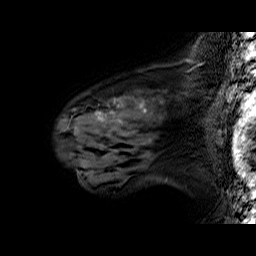
Breast MRI (dynamic contrast-enhanced), one sagittal slice. Slice 44 of 60 in the series (ordered by position). Dynamic contrast-enhanced series, time point 2 of 6 at this slice position (early post-contrast). 1.5 T. TE 6.4 ms, TR 32.9 ms. 4 mm slice thickness. 256 × 256 image matrix, field of view 200 × 200 mm. Female patient. Case-level facts recorded for this patient, not image findings: setting: breast cancer imaged before/during neoadjuvant chemotherapy; receptor status: HER2-positive.
Outlined on this slice (semi-automatically segmented with operator editing):
- analysis volume of interest (the breast-tissue region the enhancement analysis was run in; not a lesion): box from (x=57, y=78) to (x=196, y=160) px
- tumour enhancement mask (voxels above the 100 % enhancement threshold inside the analysis volume of interest): (x=95, y=102)–(x=152, y=121)